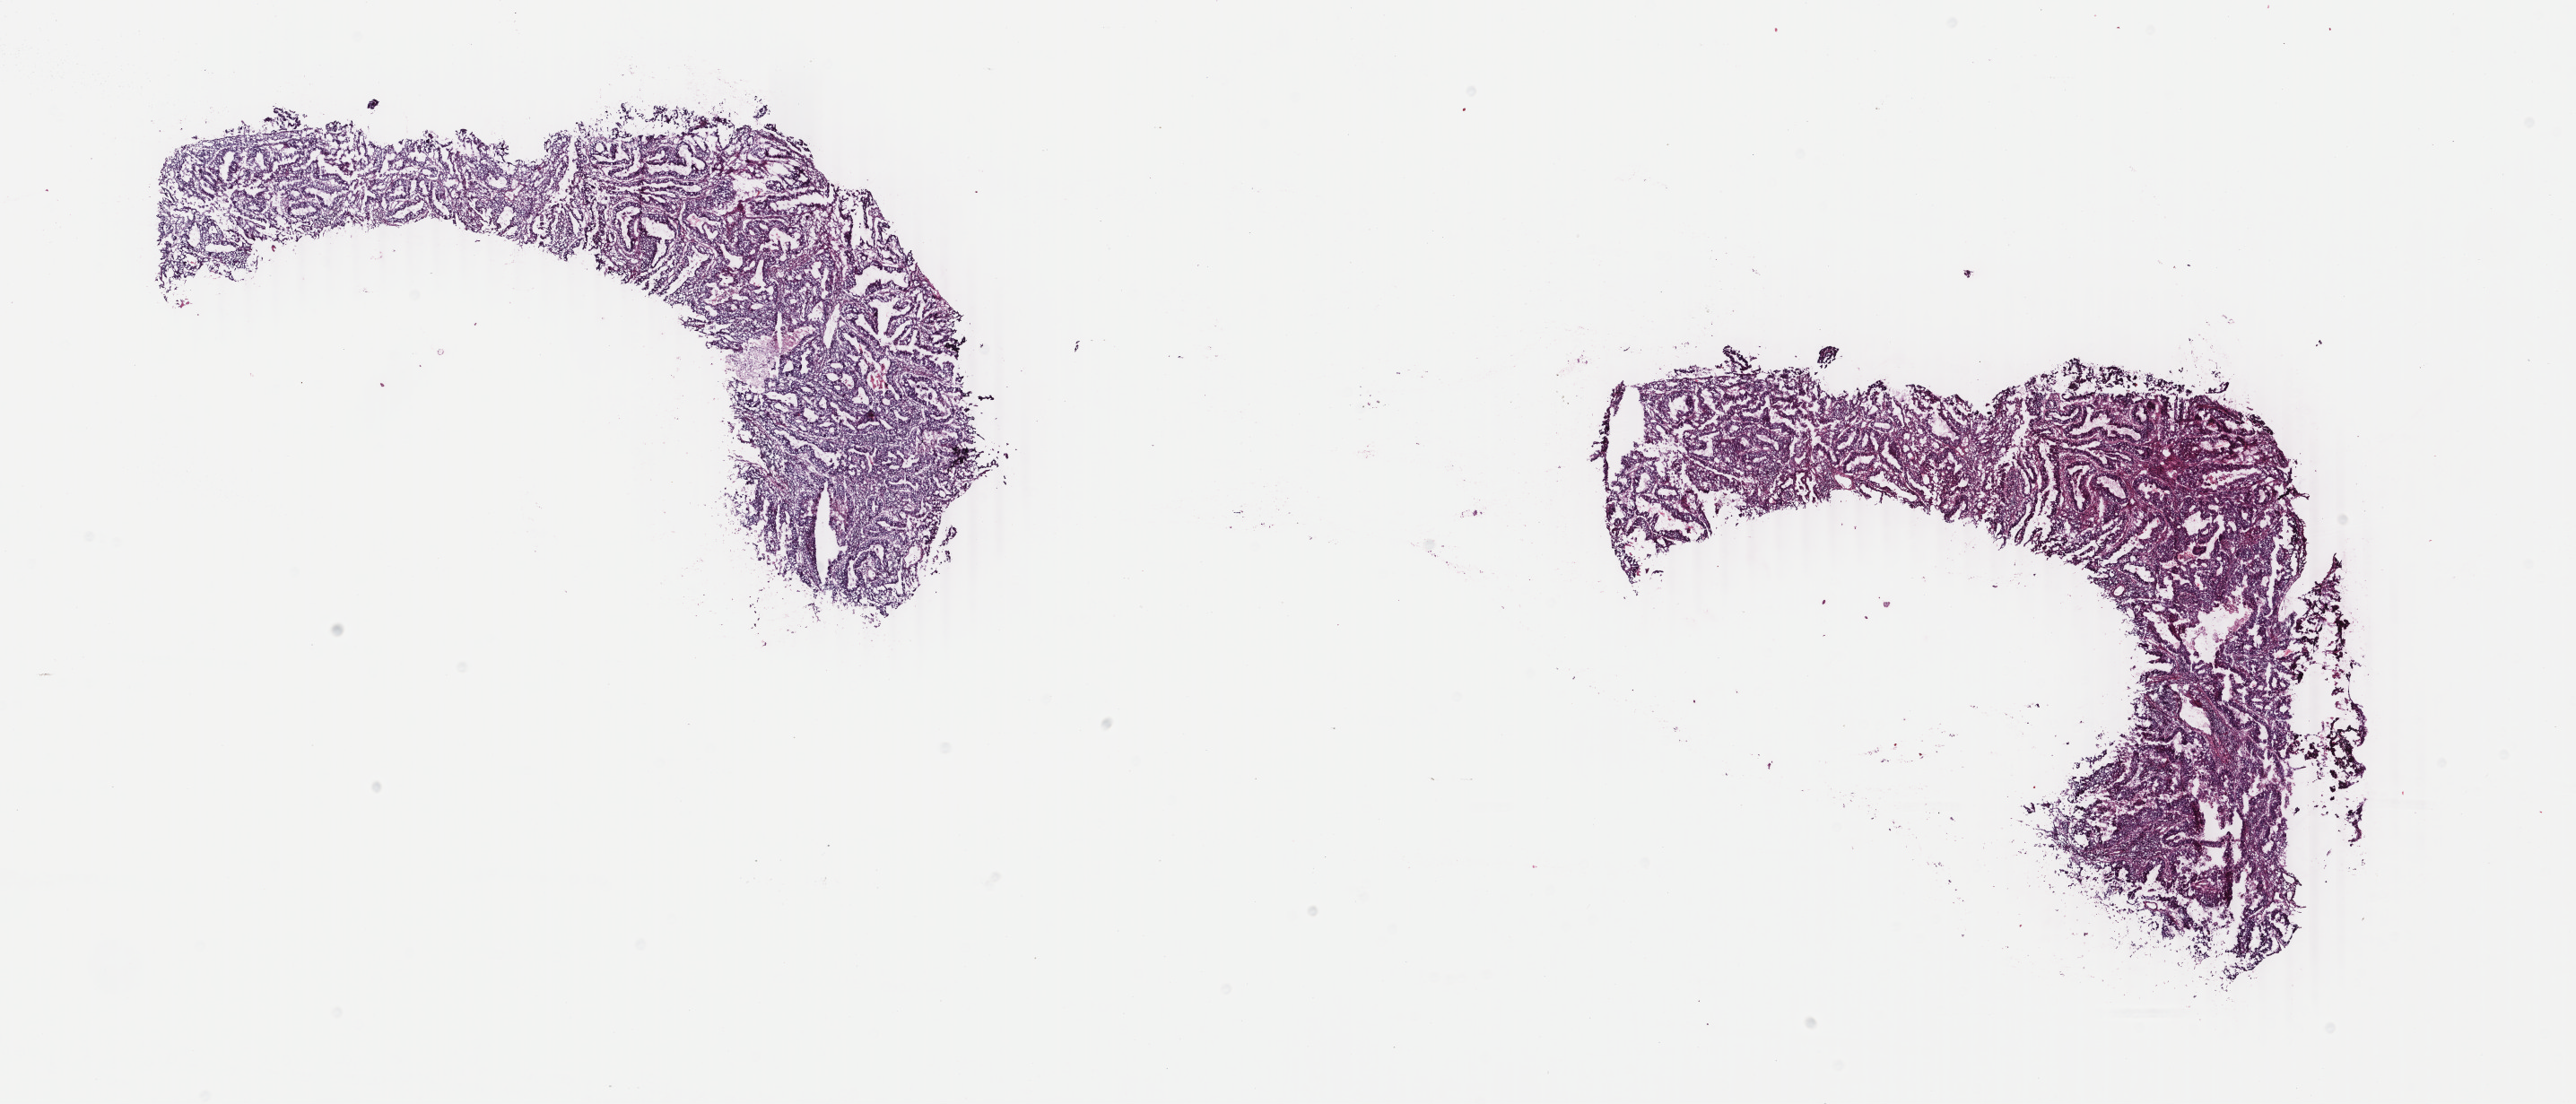
H&E-stained whole-slide image — whole scanned area (about 22.8 x 9.8 mm) shown as a low-resolution overview. Frozen section. Sample: primary tumour, uterus. Female patient; age at initial diagnosis 55 years. Histologic grade: G2 (moderately differentiated). Slide review estimates, as recorded: tumour cells 70%, tumour nuclei 70%, normal cells 0%, stromal cells 25%, necrosis 5%. Infiltration values recorded for this section: lymphocyte infiltration 40%, monocyte infiltration 30%, neutrophil infiltration 30%.
FIGO stage: IA. Pathologic diagnosis: Endometrioid adenocarcinoma, NOS (endometrium).